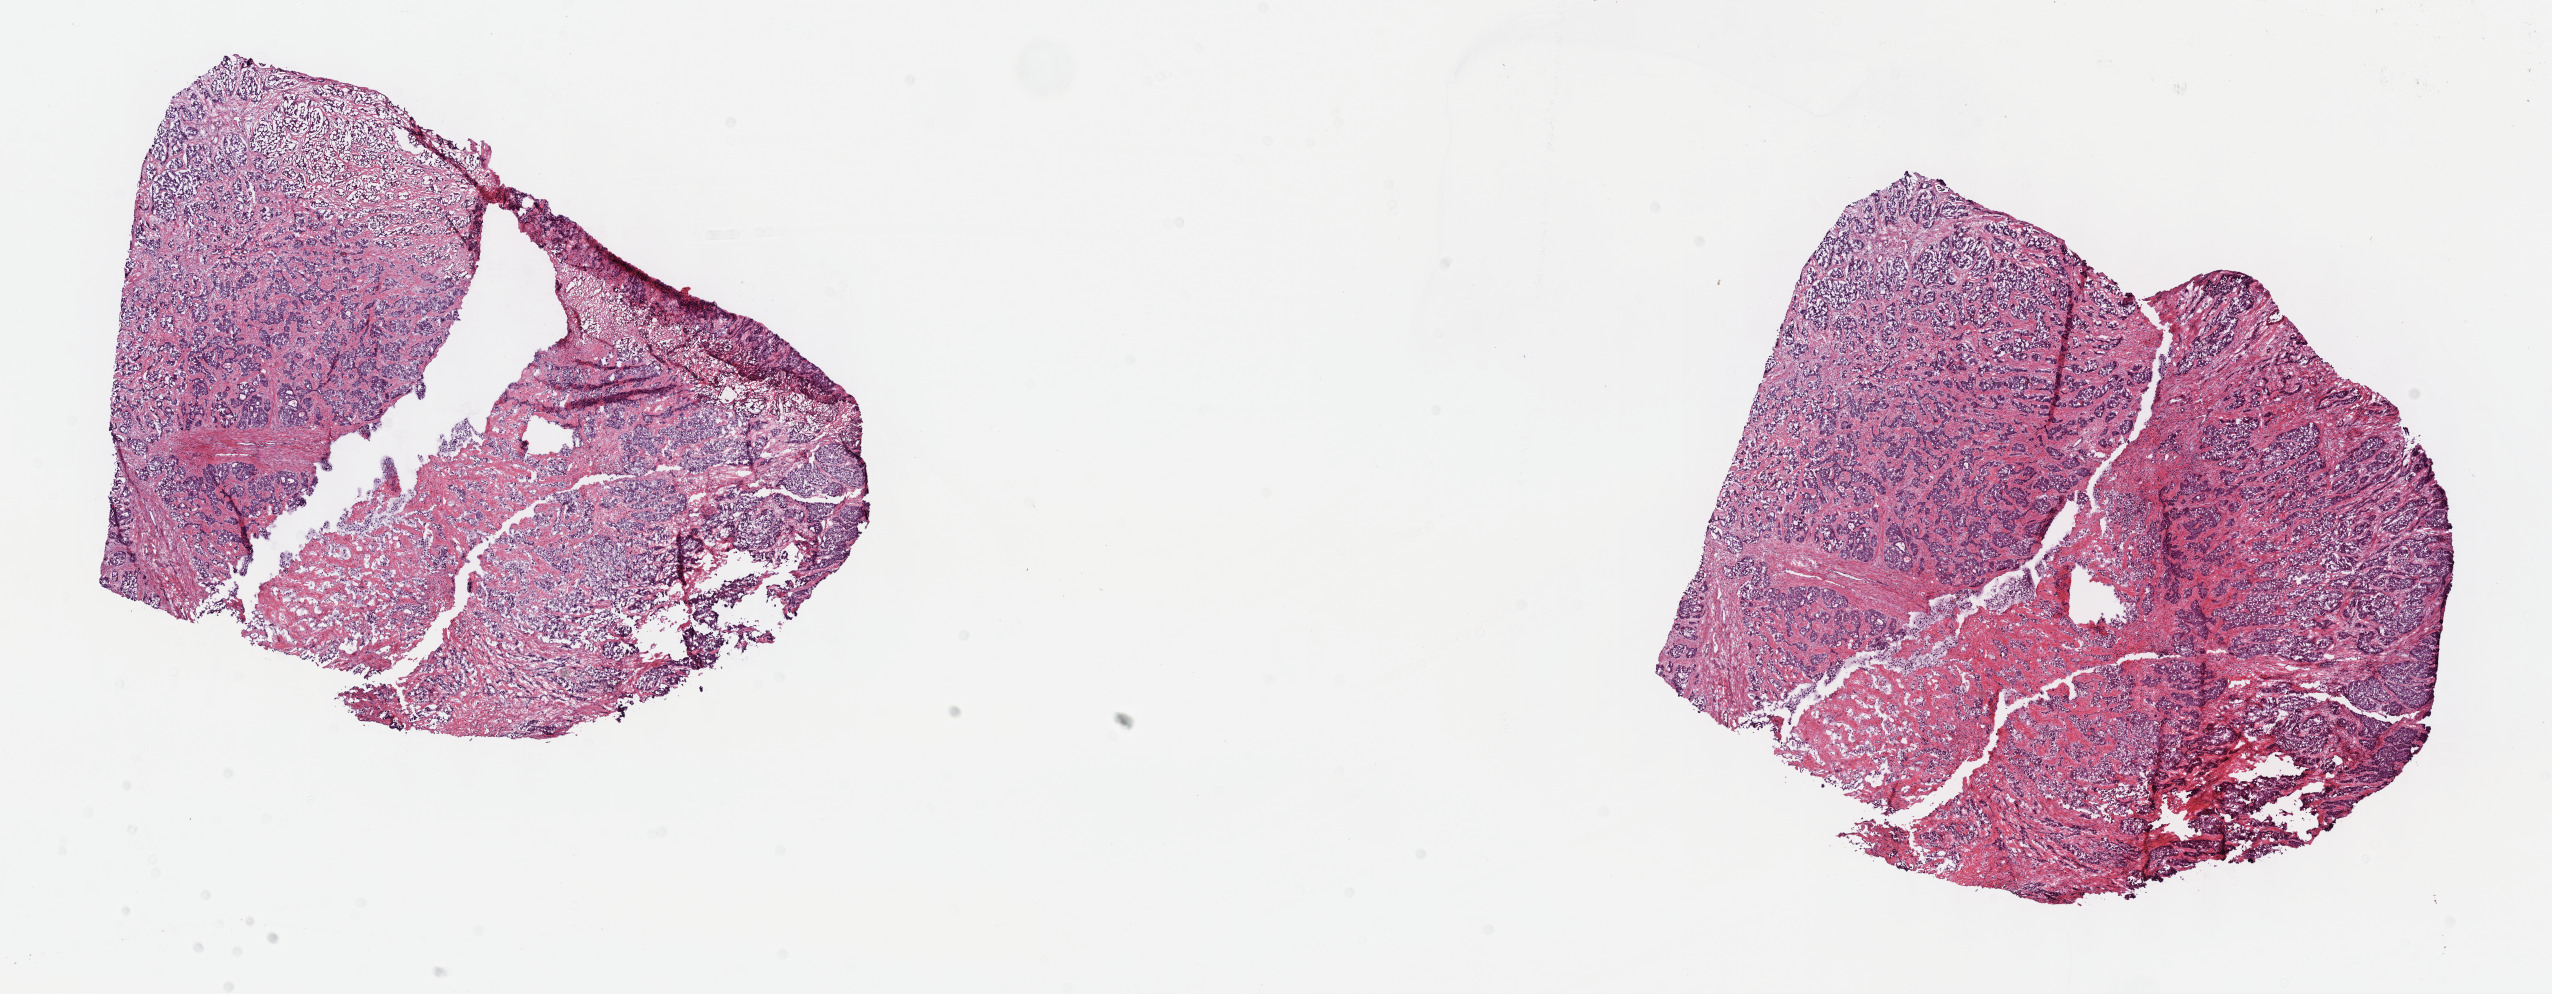
Hematoxylin and eosin (H&E) stained whole-slide image, shown as a low-resolution overview of the whole scanned area (about 20.6 x 8.0 mm), frozen section from the top of the tissue portion, sample: primary tumour, liver. Patient: male, age at initial diagnosis 70 years. Histologic grade: G2 (moderately differentiated). Slide review estimates, as recorded: tumour cells 100%, tumour nuclei 70%, normal cells 0%, stromal cells 0%, necrosis 0%. Inflammatory infiltration, as recorded: lymphocyte infiltration 3%, monocyte infiltration 0%, neutrophil infiltration 0%.
• pathologic diagnosis: Hepatocellular carcinoma, NOS
• AJCC pathologic stage: I (7th edition)